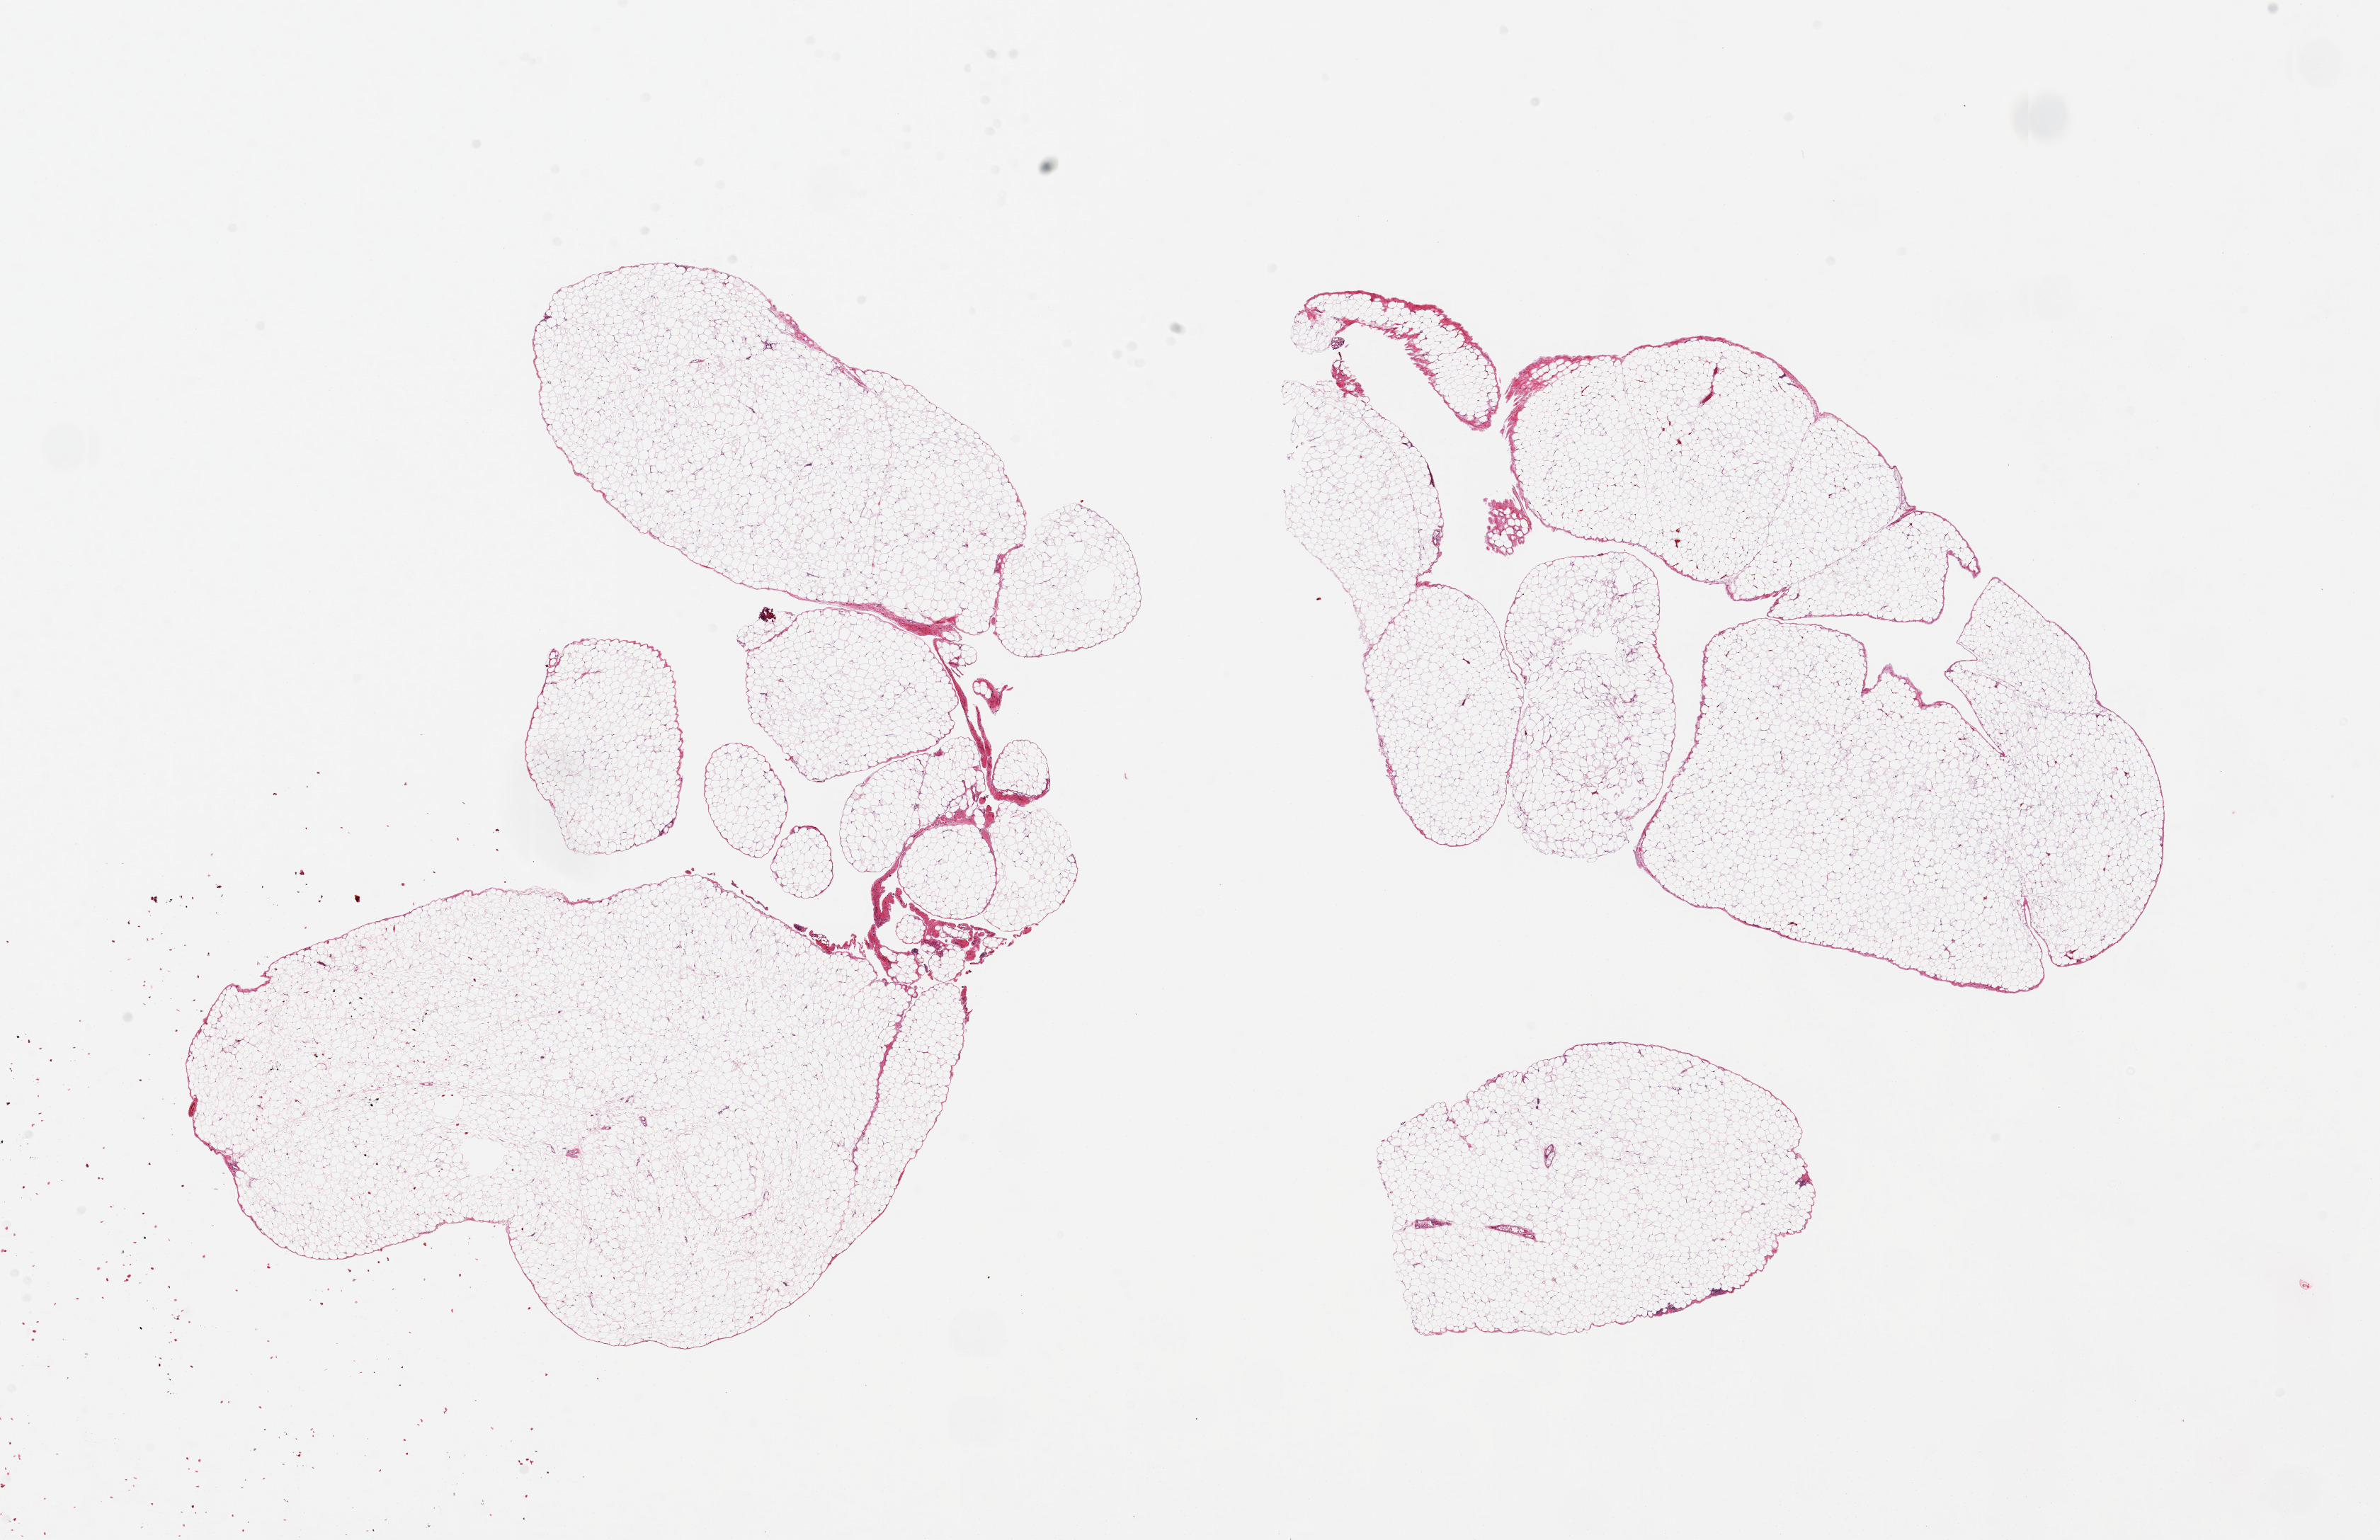
Digitized H&E-stained section — shown as a low-resolution overview of the whole scanned area (about 26.6 x 17.2 mm, slide scanned at 20x). PAXgene-fixed, paraffin-embedded tissue. Target tissue: omentum. Tissue donor sample. Donor sex: male.
- reviewer comment on this tissue sample: 2 pieces, 12x8 & 11.5x11.5mm; No artifacts